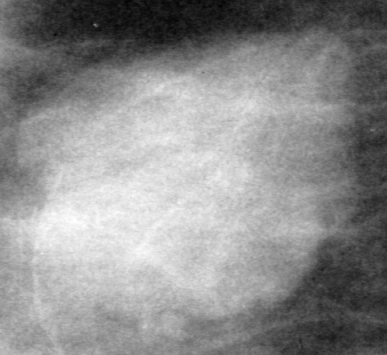
Region of interest cut from a scanned film mammogram (one marked finding), left breast, MLO view.
- Mass, shape oval, margins ill defined; BI-RADS assessment category 4; pathology (as recorded): benign.